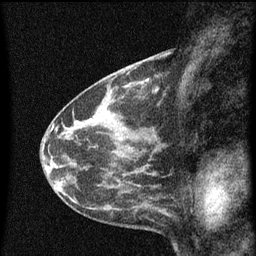
Breast MRI (dynamic contrast-enhanced), one sagittal slice. Position 26 of 60 along the scan axis. Dynamic contrast-enhanced series, image 2 of 3 at this slice position (ordered by acquisition). 1.5 T. TE 4.2 ms, TR 8 ms. 2 mm slice thickness. 256 × 256 image matrix, field of view 180 × 180 mm. Patient: female, 41 years.
Structures marked on this image (semi-automatically segmented with operator editing):
- analysis volume of interest (the breast-tissue region the enhancement analysis was run in; not a lesion): bounding box (x1, y1, x2, y2) in pixels: (130, 76, 157, 99)
- tumour enhancement mask (voxels above the 70 % enhancement threshold inside the analysis volume of interest): (140, 78, 157, 93)